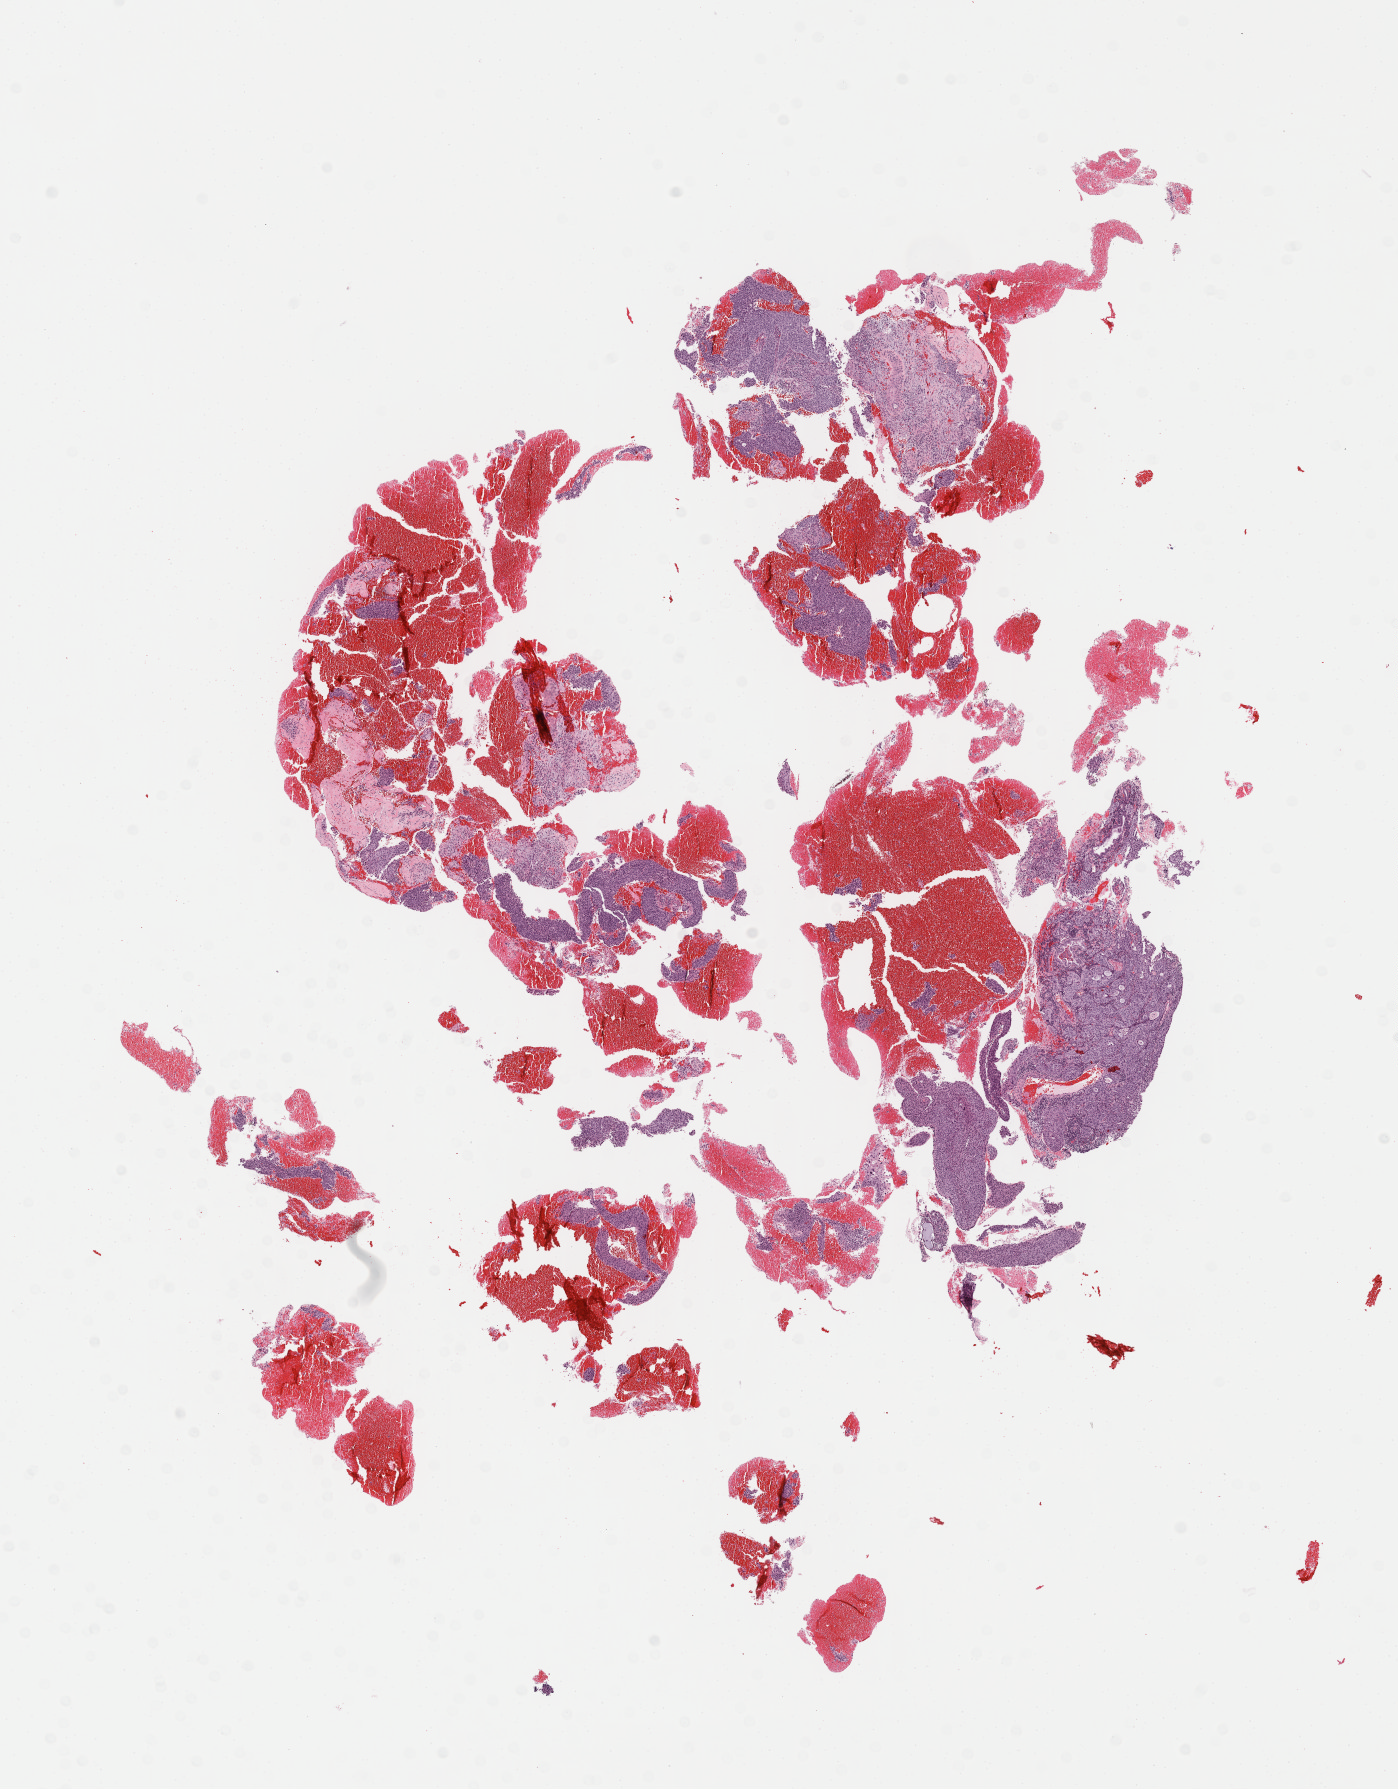
Digitized H&E-stained tissue section (whole slide), shown as a low-resolution overview of the whole scanned area (about 11.0 x 14.1 mm, from a 40x scan). Formalin-fixed paraffin-embedded (FFPE) diagnostic section. Primary tumour sample from the cervix. Patient: female, age at initial diagnosis 56 years.
Diagnosis: Squamous cell carcinoma, NOS (cervix uteri).